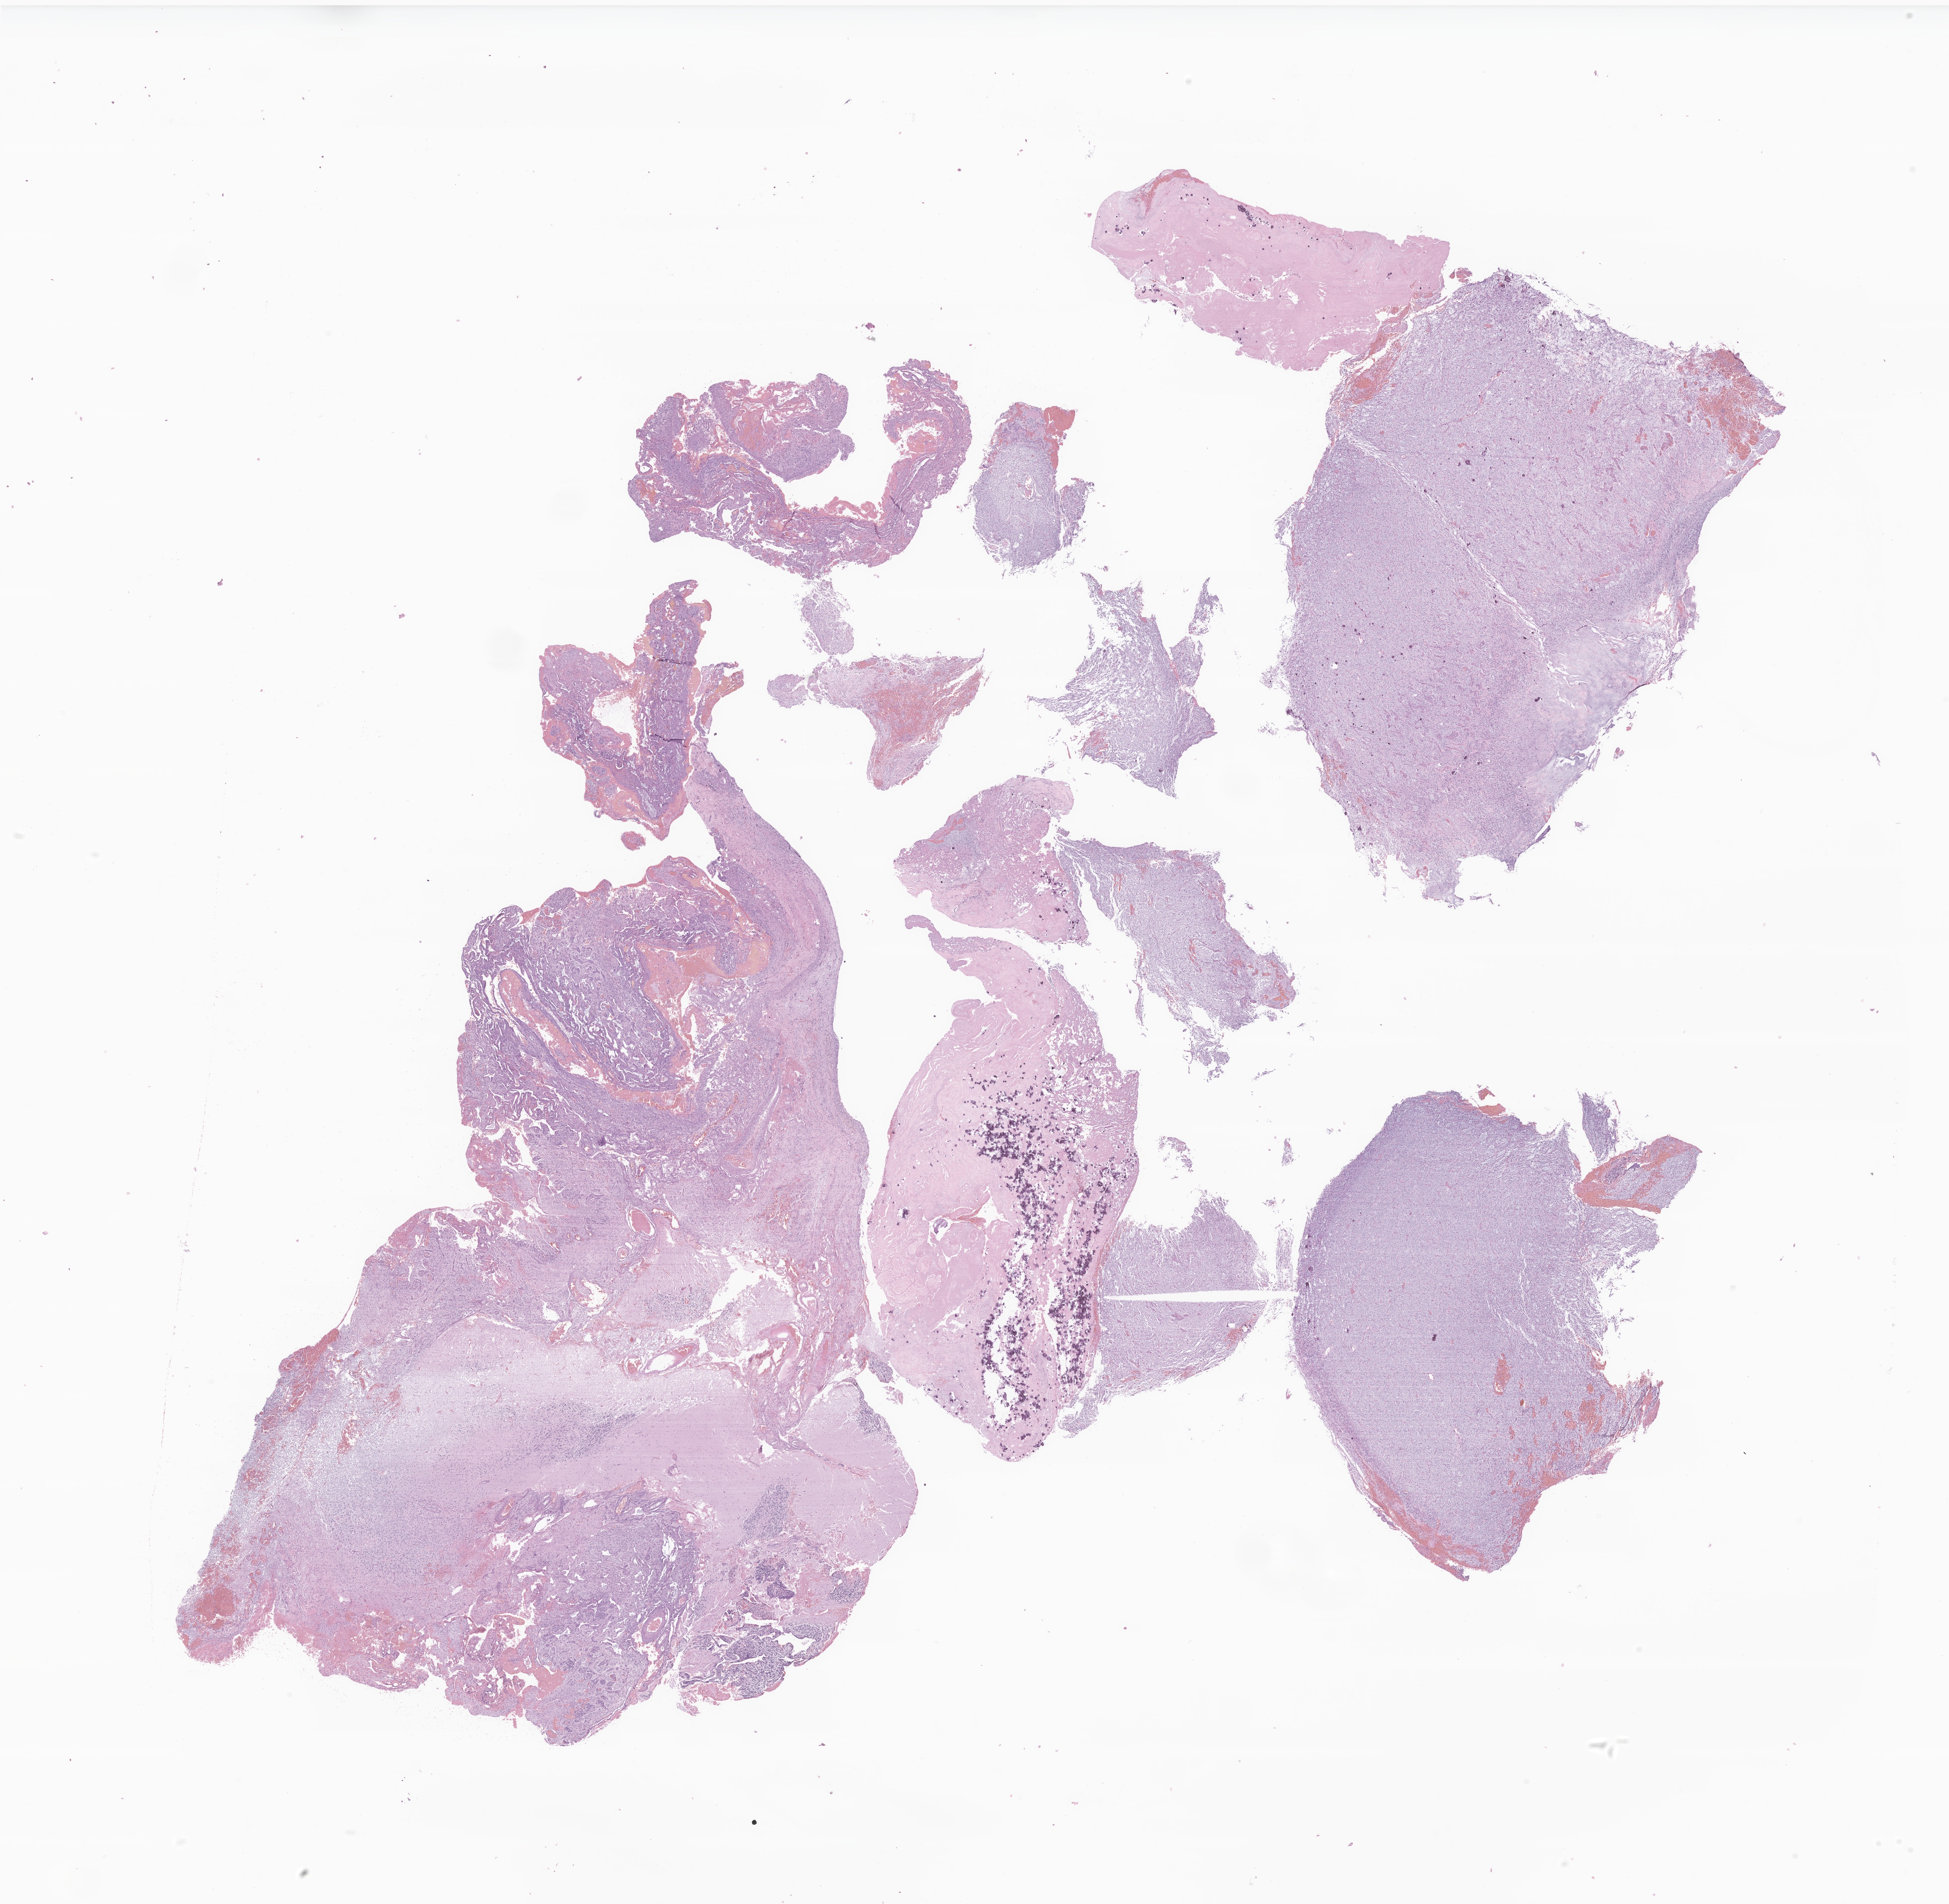
H&E whole-slide image of tumor tissue from the brain, a low-resolution overview of the entire scanned area, about 23.3 x 22.8 mm; FFPE section. Female patient, age 128 months (10 years 8 months).
Diagnosis: Pilocytic astrocytoma.